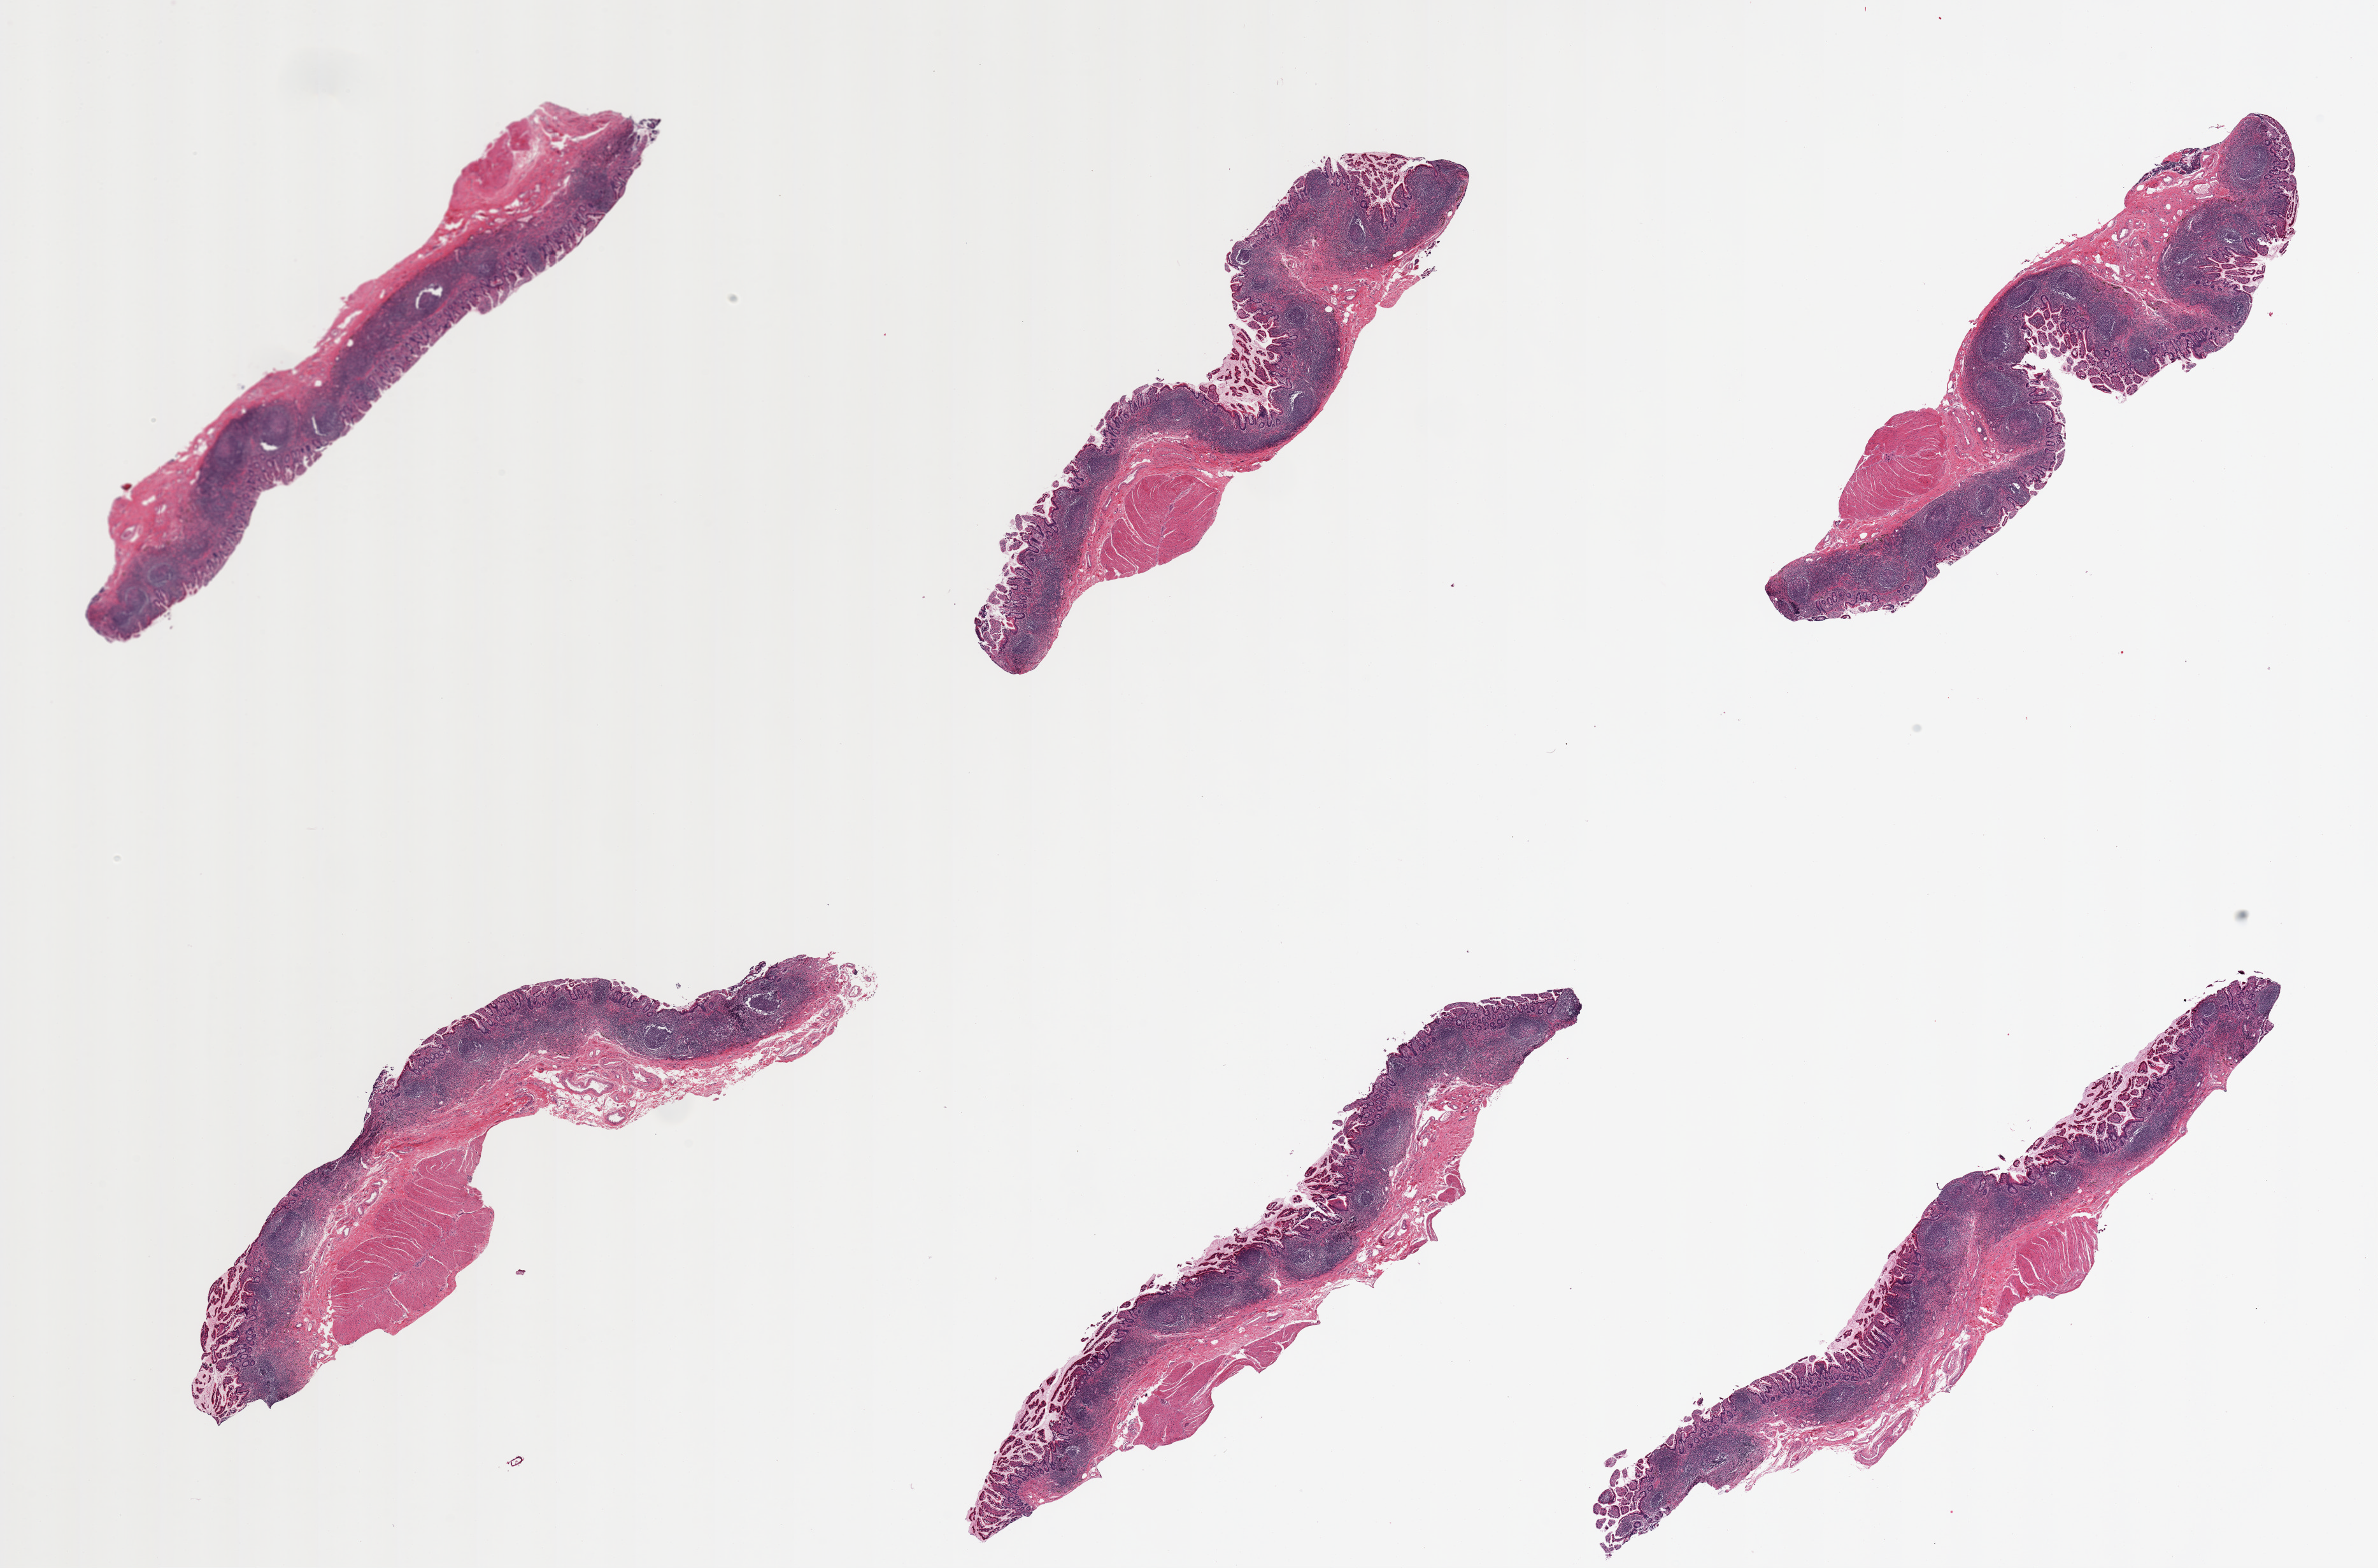
Digitized haematoxylin and eosin-stained section — a low-resolution overview of the entire scanned area, about 29.5 x 19.5 mm (acquisition: 20x scan). PAXgene-fixed, paraffin-embedded tissue. Section of ileum (target tissue). Donor tissue sample. Female donor.
Review note (as recorded): 6 pieces; Mucosa with some muscularis propria; Plenty of mucosal lymphoid tissue; Superficial mucosa is sloughed.